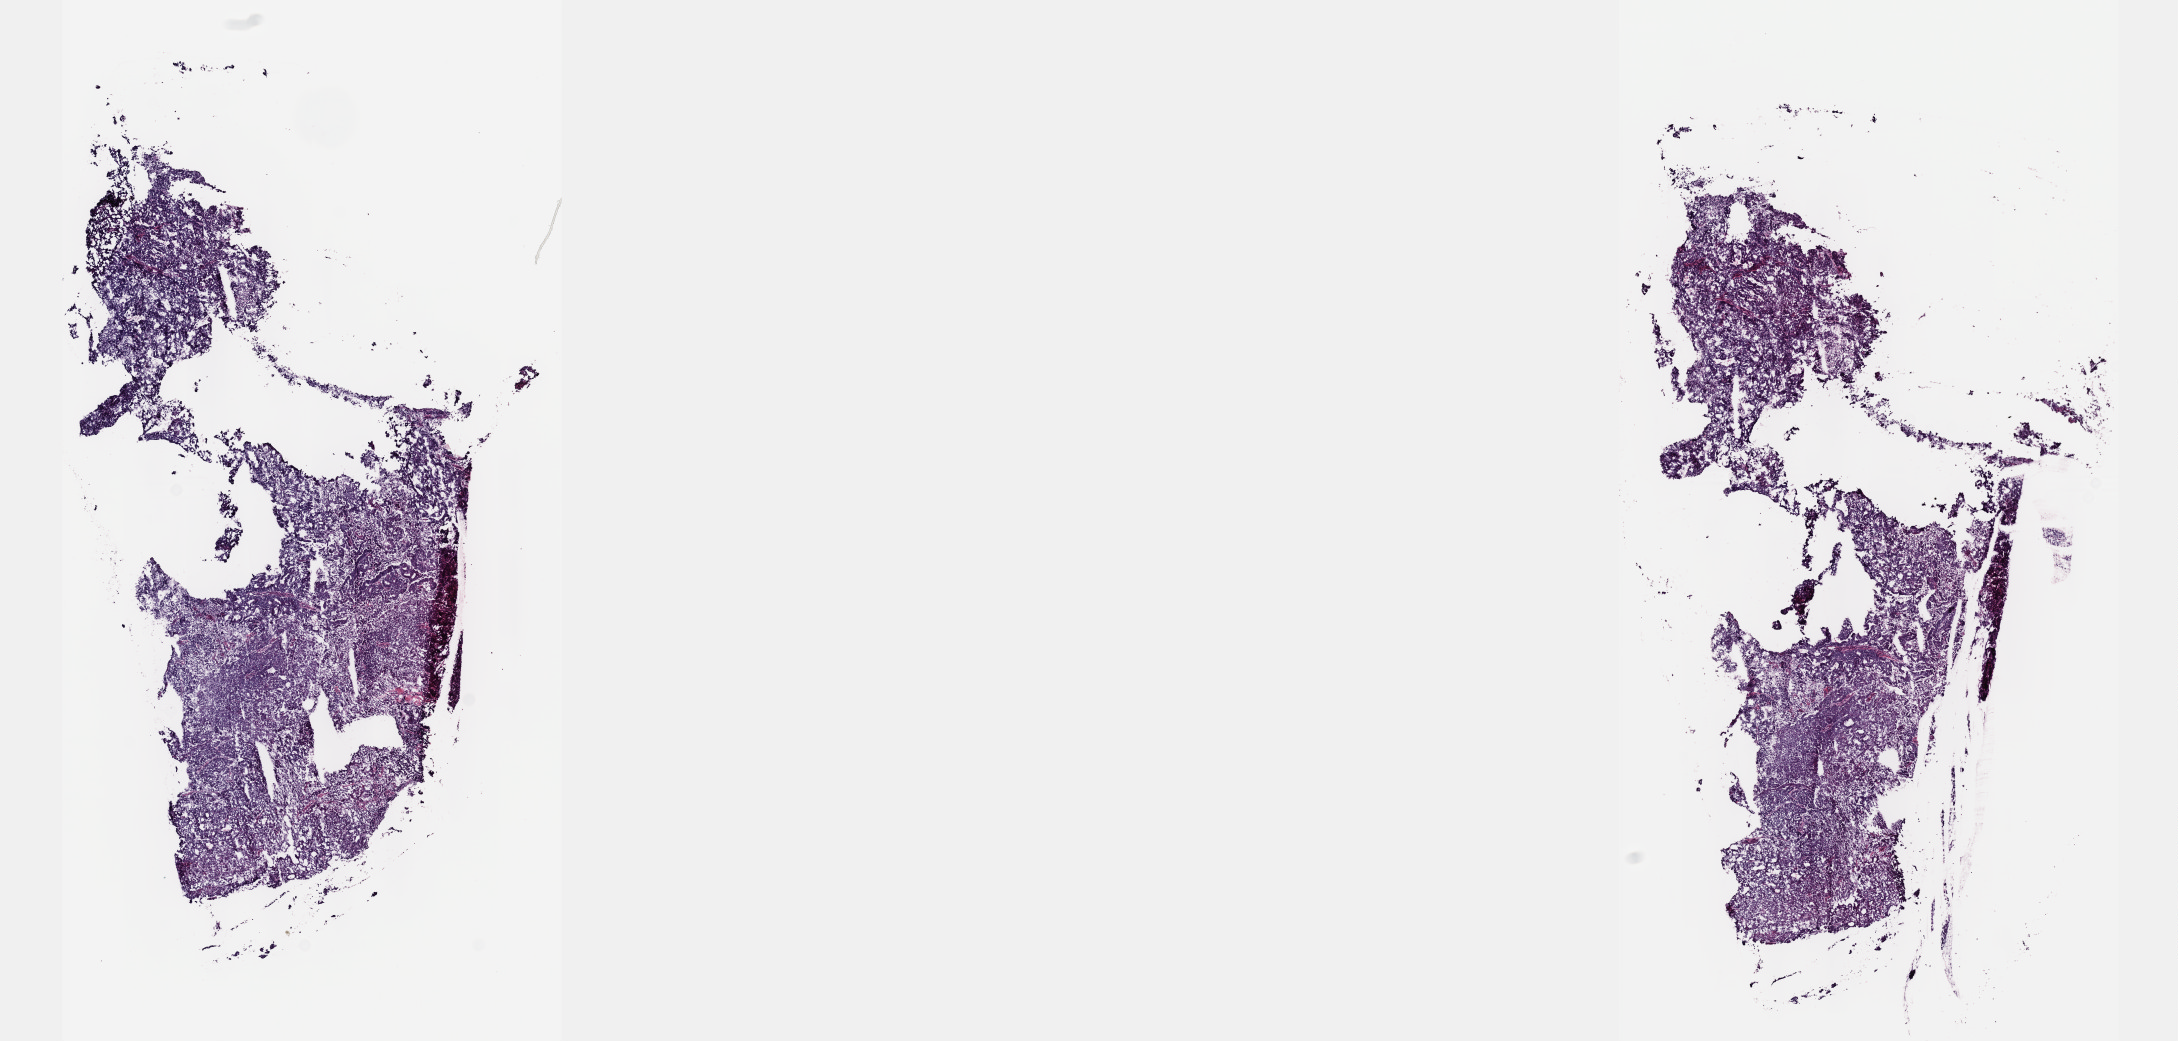
Hematoxylin and eosin (H&E) stained whole-slide image, a low-resolution overview of the entire scanned area, about 17.6 x 8.4 mm (from a 40x scan); frozen section; primary tumour sample from the uterus. Female patient; age at initial diagnosis 64 years. Composition of this section per pathologist review: tumour cells 70%, tumour nuclei 70%.
Histologic diagnosis: Endometrioid adenocarcinoma, NOS (endometrium).